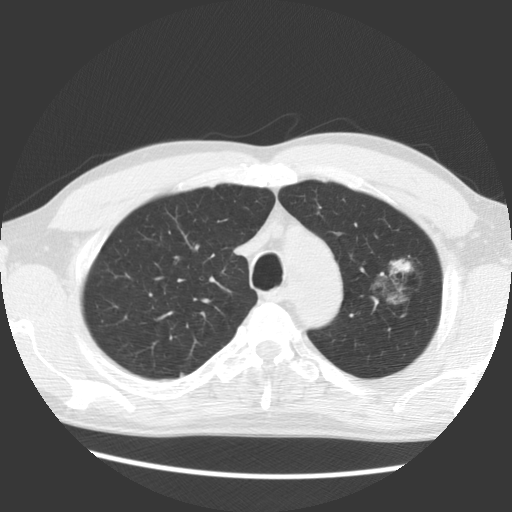
Low-dose screening chest CT, axial slice; baseline screening round; lung window (W 1500 / L -600 HU); standard (soft-tissue) reconstruction kernel (STANDARD); slice 106 of 138 in the series; 512 × 512 image matrix. Male, age 61 years at enrolment.
Lesion marked by an expert reader, bounding box [x1, y1, x2, y2] px = [351, 243, 436, 323]. The exam's reader record, not a measurement of the box and not confirmed to be the same lesion: non-calcified nodule or mass ≥4 mm, left upper lobe, 17 × 14 mm, soft tissue attenuation. Official screen result: positive, change unspecified: nodule(s) >= 4 mm or enlarging nodule(s), mass(es), or other non-specific abnormalities suspicious for lung cancer.